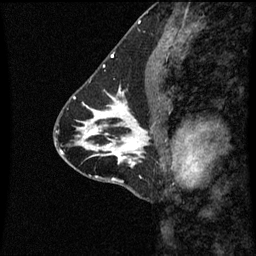
Breast MRI (dynamic contrast-enhanced), one sagittal slice. Position 29 of 60 along the scan axis. Dynamic contrast-enhanced series, image 2 of 3 at this slice position (ordered by acquisition). 1.5 T. TE 4.2 ms, TR 8.9 ms. 2 mm slice thickness. 256 × 256 image matrix, field of view 200 × 200 mm. Female patient, age 43 years. From the clinical record (not read from this slice): setting: breast cancer imaged before/during neoadjuvant chemotherapy; receptor status: HR-positive, HER2-negative.
Structures marked on this image (semi-automatically segmented with operator editing):
- analysis volume of interest (the breast-tissue region the enhancement analysis was run in; not a lesion): box from (x=110, y=100) to (x=164, y=163) px
- tumour enhancement mask (voxels above the 70 % enhancement threshold inside the analysis volume of interest): (x=110, y=128)–(x=143, y=163)